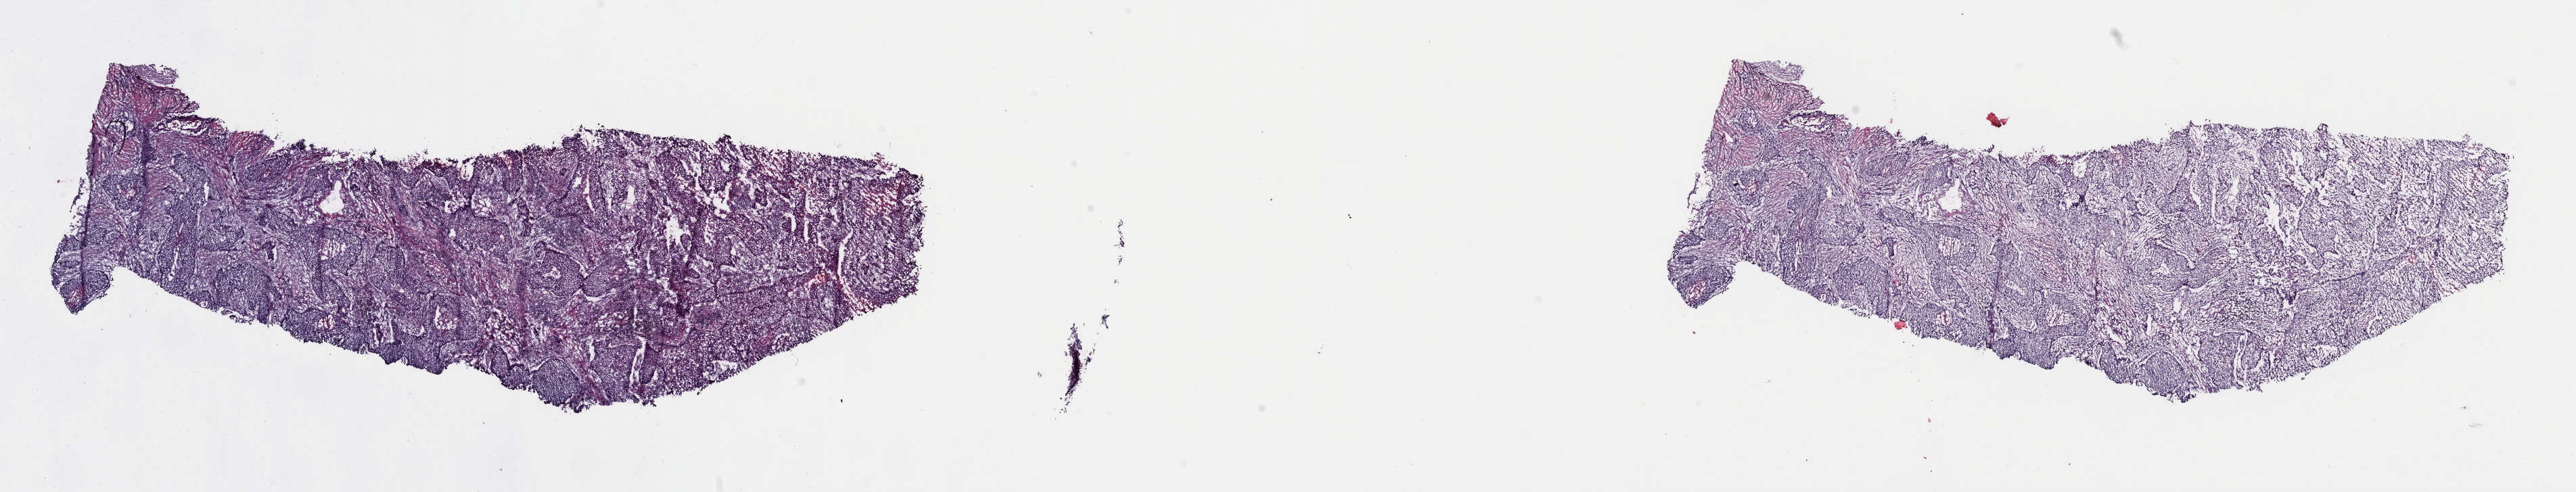
H&E-stained whole-slide image, whole scanned area (about 30.1 x 5.7 mm, slide scanned at 40x) shown as a low-resolution overview, frozen section from the top of the tissue portion, primary tumour sample from the lung. Female, age 56 years at initial diagnosis. Slide review estimates, as recorded: tumour cells 95%, tumour nuclei 75%, normal cells 0%, stromal cells 0%, necrosis 5%. Inflammatory infiltration, as recorded: lymphocyte infiltration 0%, monocyte infiltration 0%, neutrophil infiltration 0%.
AJCC pathologic stage: IIB (7th edition). Histologic diagnosis: Squamous cell carcinoma, NOS (lower lobe, lung).